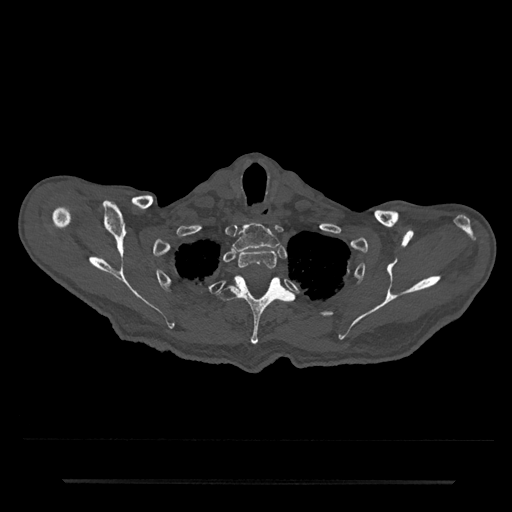
CT including the spine, one axial slice; position 680 of 797 along the scan axis; reconstruction kernel Br40s/3; 120 kVp; bone window (W 1800 / L 400 HU); 0.5 mm slice thickness; 512 × 512 image matrix, field of view 427 × 427 mm. Male patient, age 74 years. From the clinical record (not read from this slice): primary cancer: prostate.
Annotated regions visible in this slice (semi-automatically segmented with operator editing):
- T1 vertebra: bounding box <232,223,280,252> (left, top, right, bottom; pixels)
- T2 vertebra: <238,249,277,270>
- T3 vertebra: <218,275,294,345>